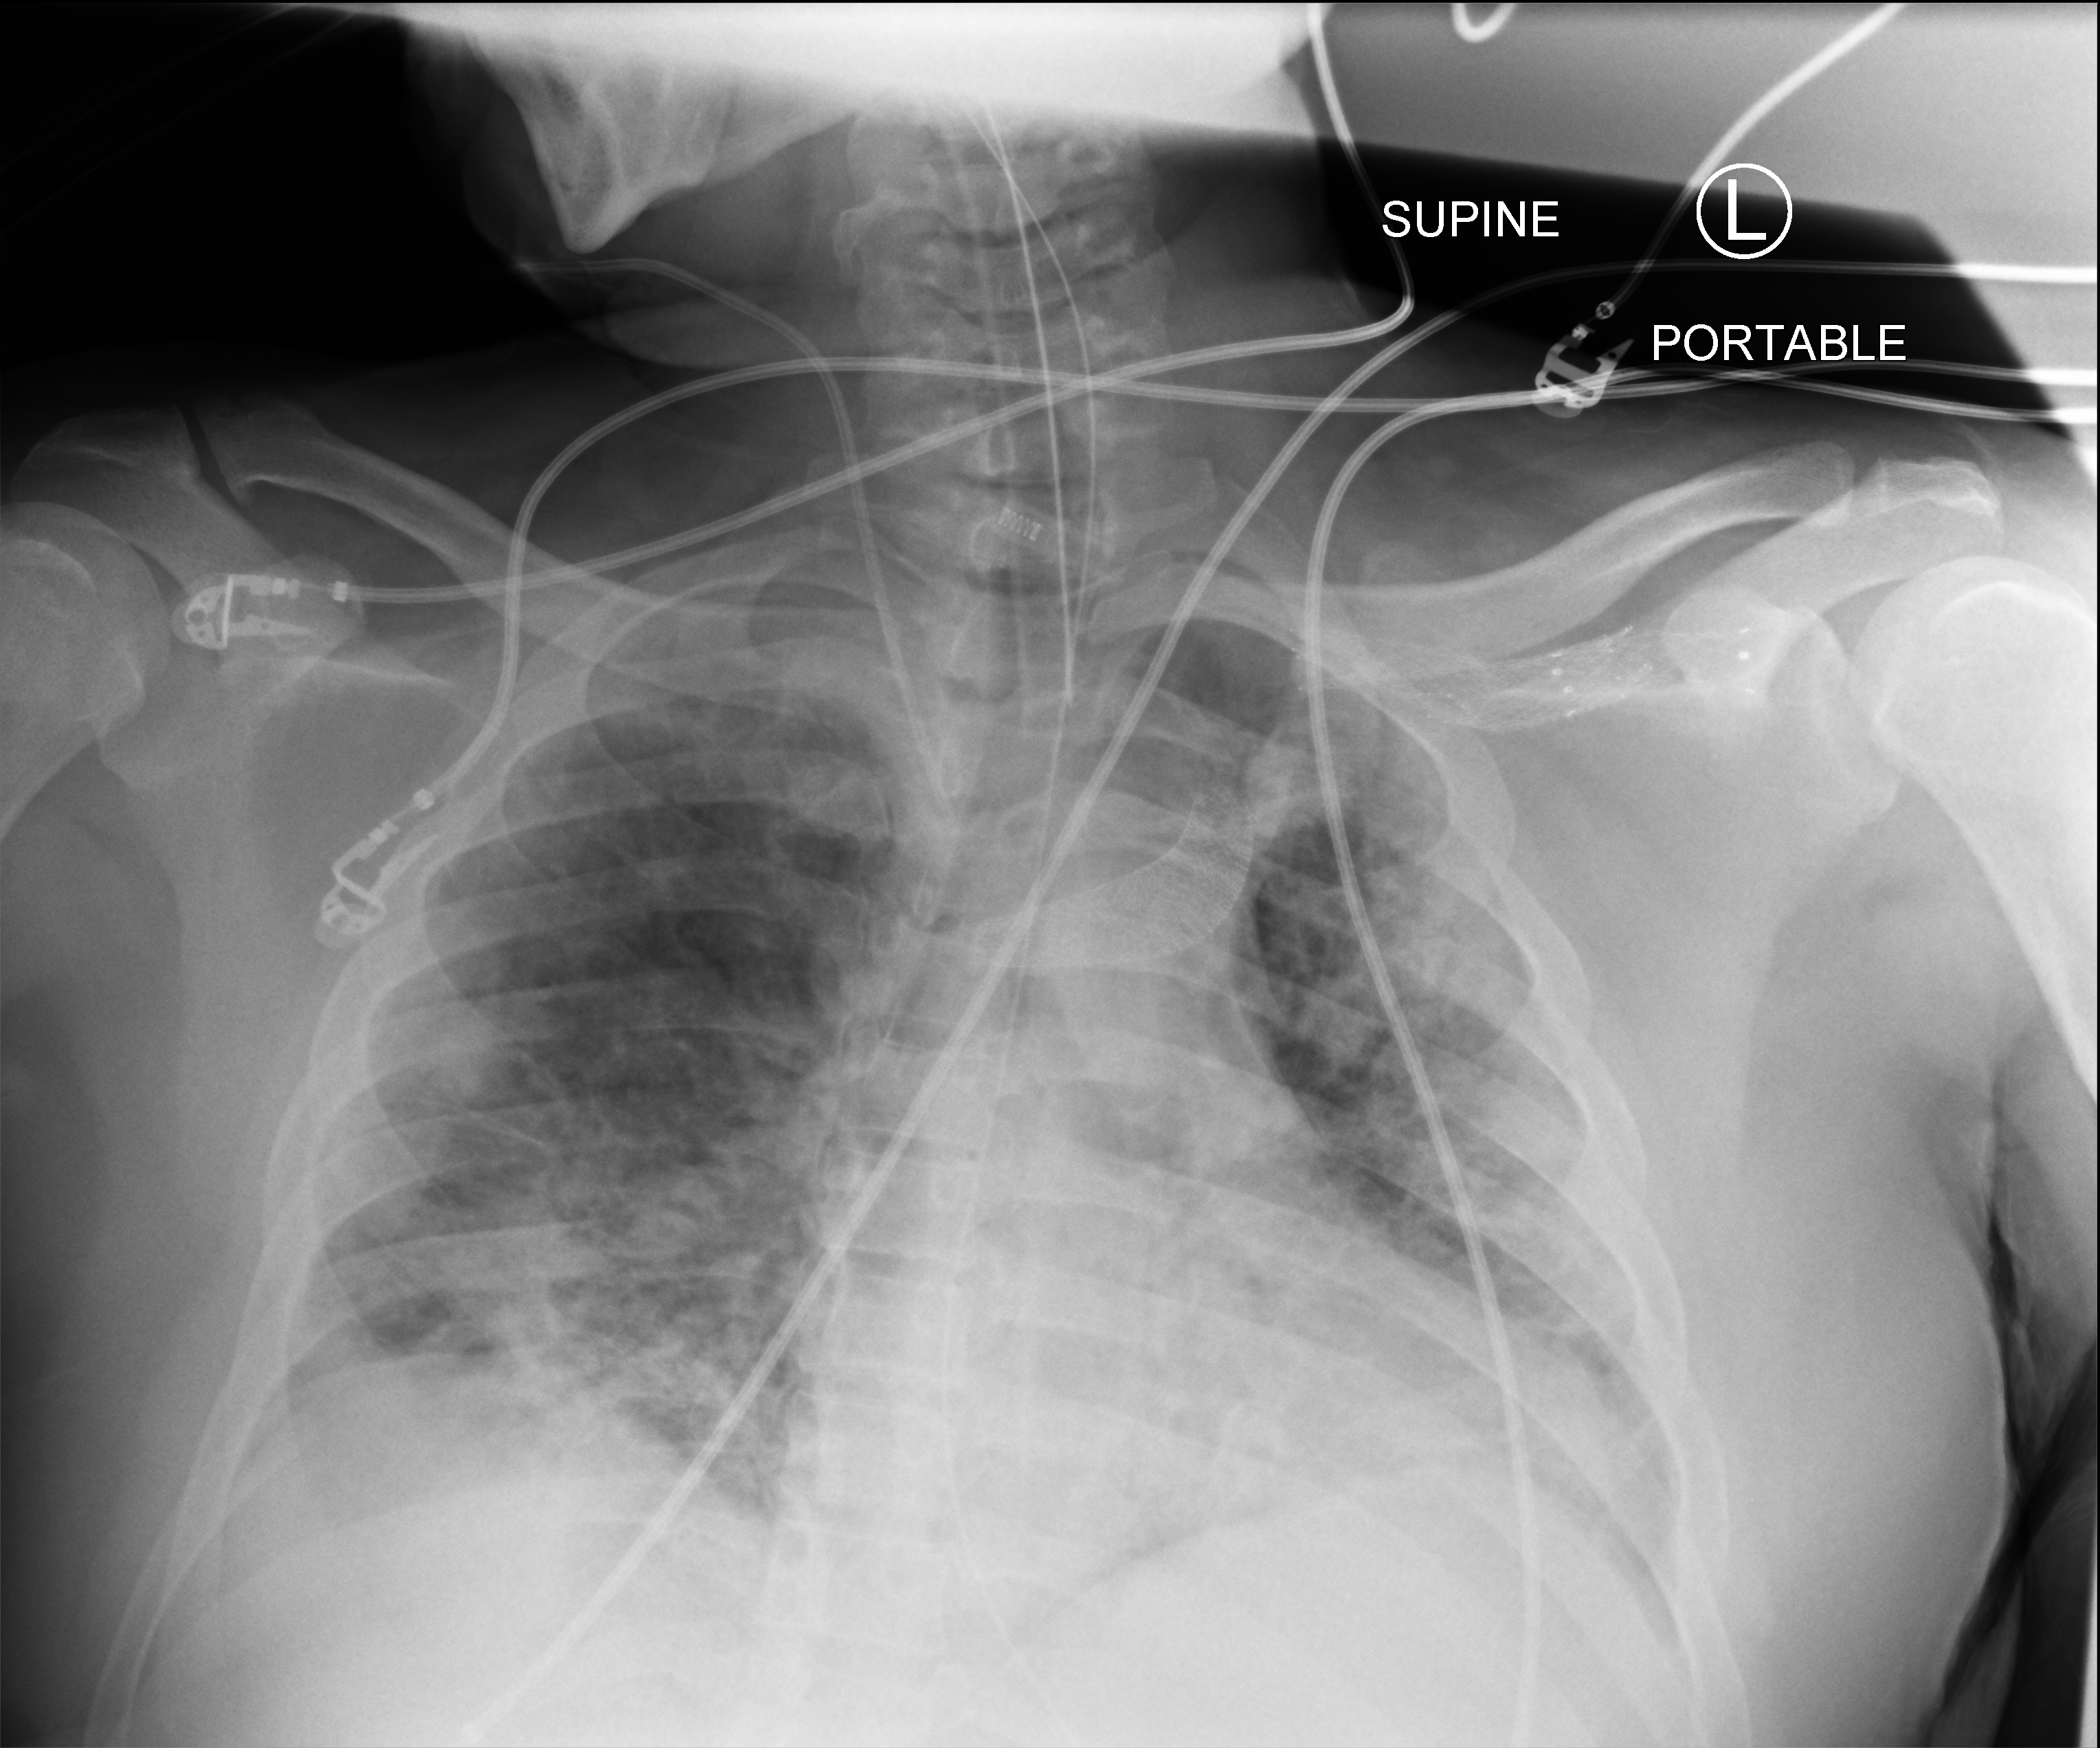
Bedside chest radiograph (computed radiography); anteroposterior (AP) projection. Patient hospitalised with COVID-19; male, aged 18–59 years.
Hospital-stay facts (about this admission, not read from this image; timing relative to this image not recorded): admitted to intensive care during this hospital stay: yes; mechanically ventilated during this hospital stay: yes.